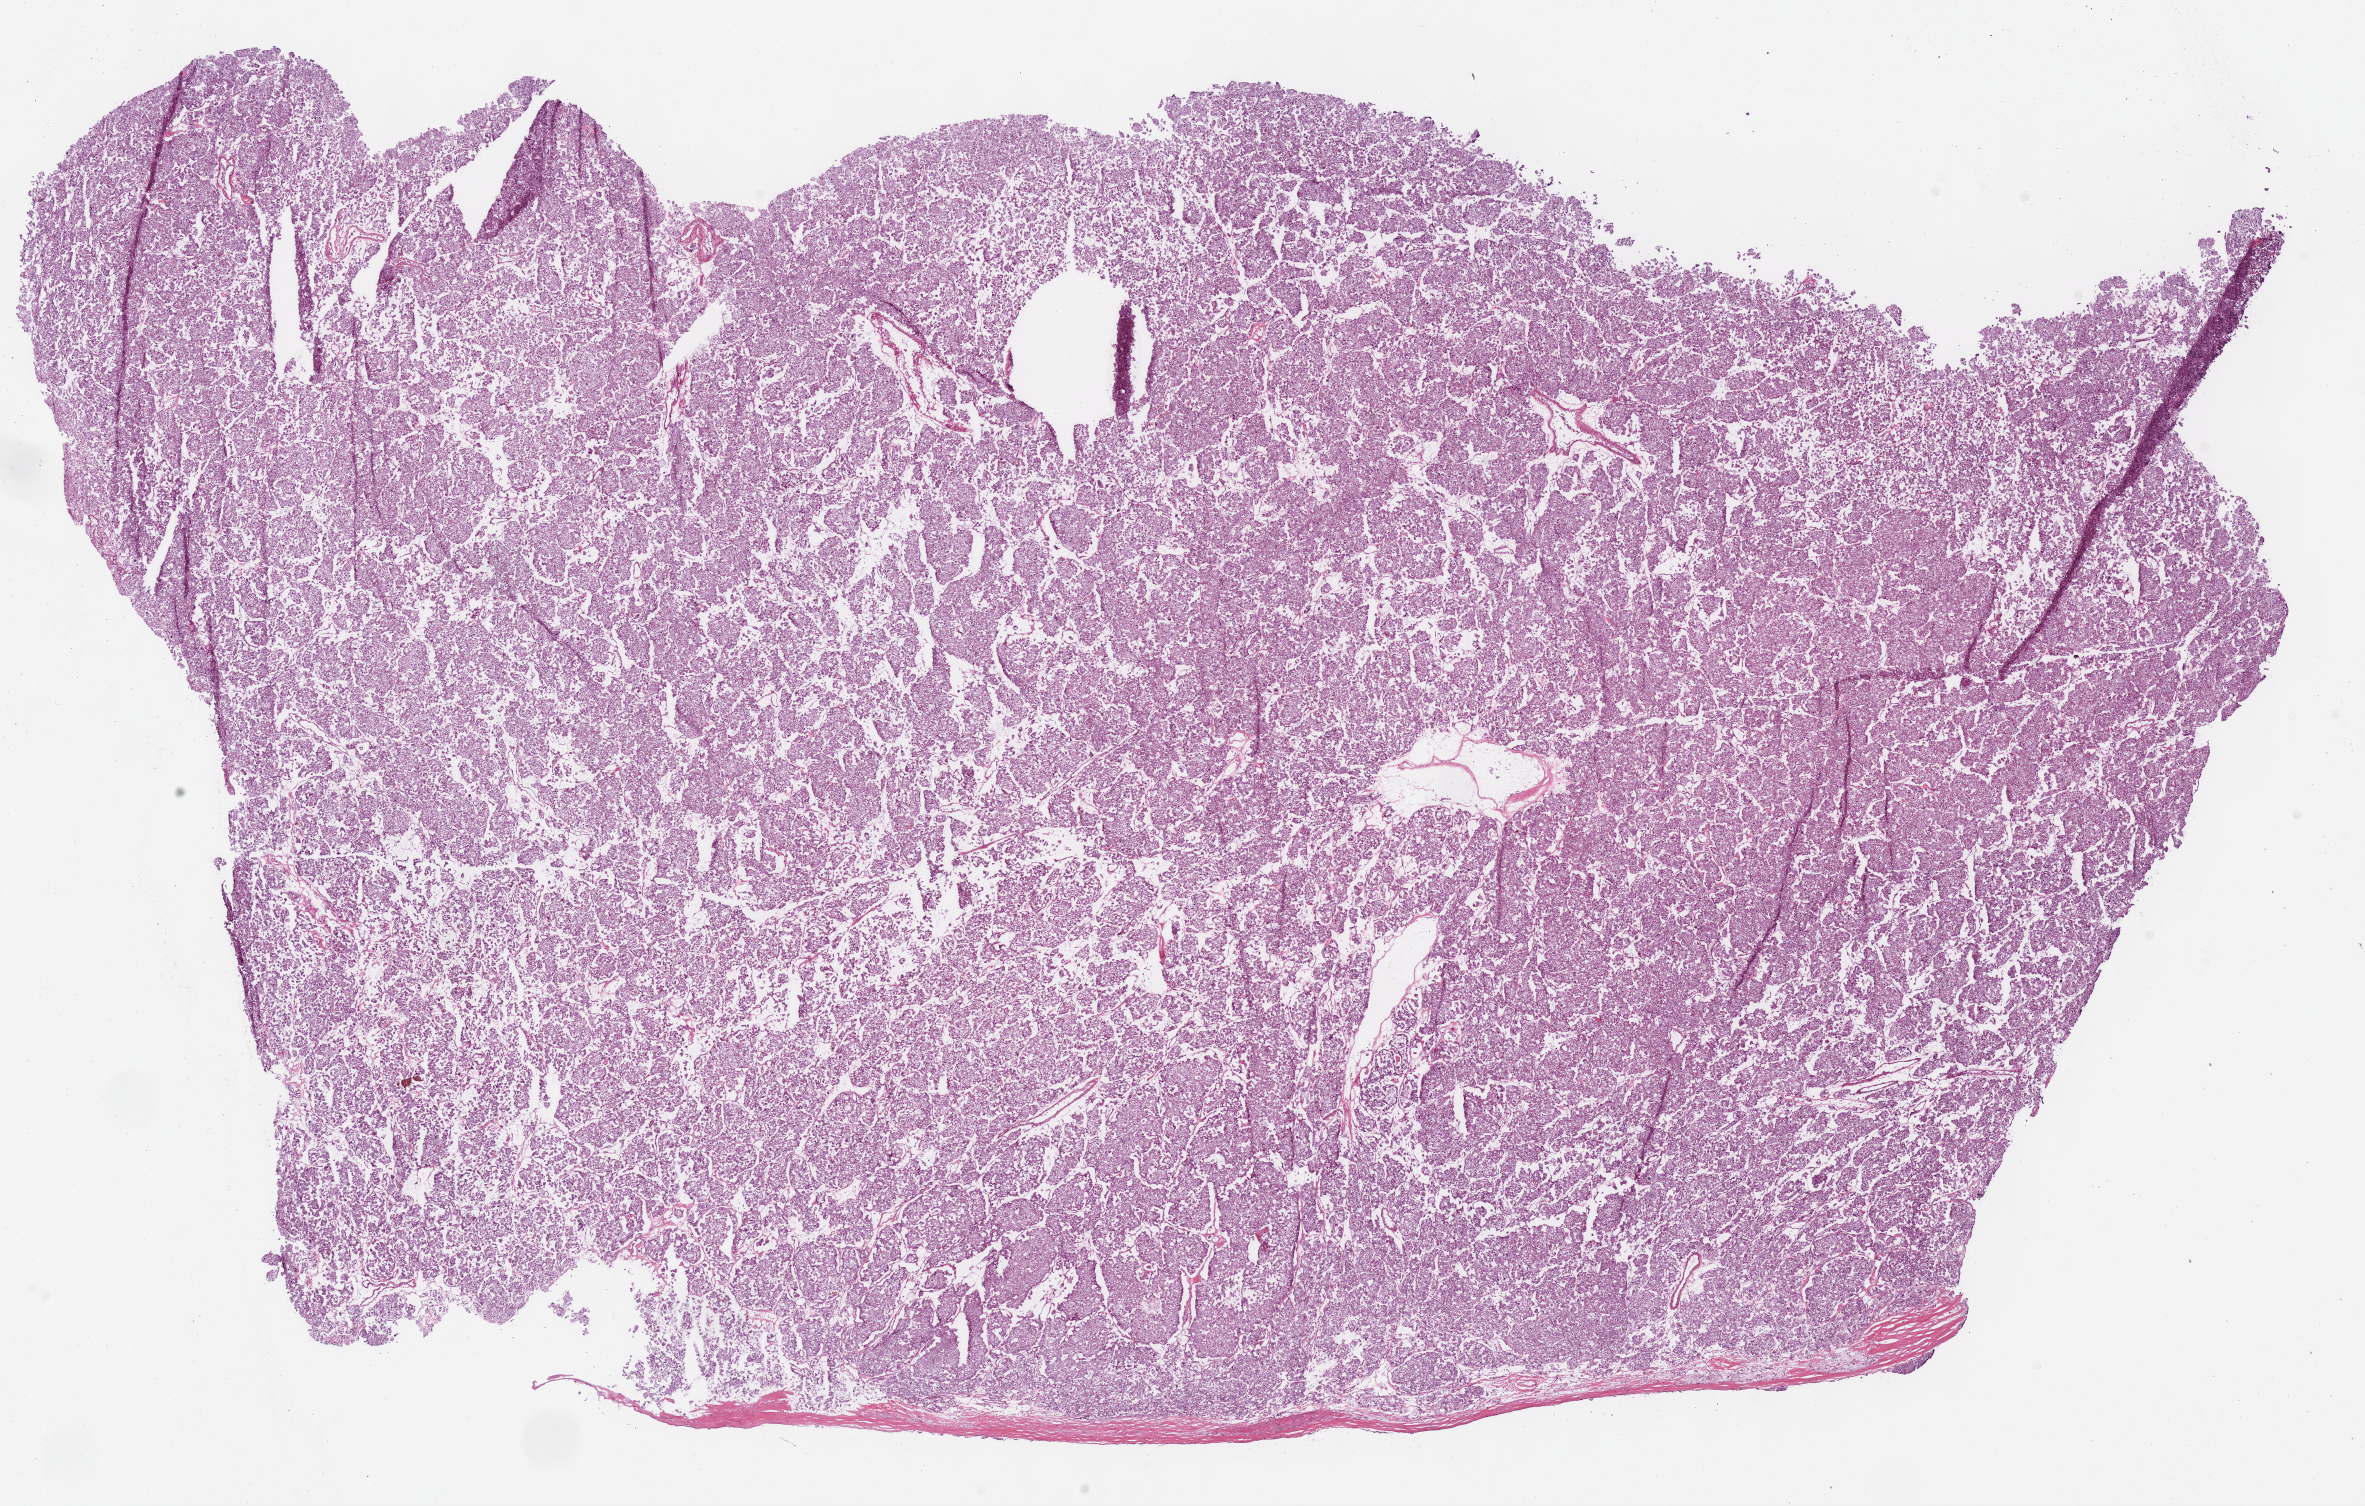
Digitized Hematoxylin and eosin (H&E) stained tissue section (whole slide), a low-resolution overview of the entire scanned area, about 18.6 x 11.8 mm; frozen section; kidney, primary tumour sample. Patient: male, age at initial diagnosis 55 years. Pathologist review of this section (percent, as recorded): tumour cells 100%, tumour nuclei 90%, normal cells 0%, stromal cells 0%, necrosis 0%. Inflammatory infiltration, as recorded: lymphocyte infiltration 2%, monocyte infiltration 0%, neutrophil infiltration 0%.
* AJCC pathologic stage: I (6th edition)
* TNM: T1b N0 M0
* histologic diagnosis: Renal cell carcinoma, chromophobe type